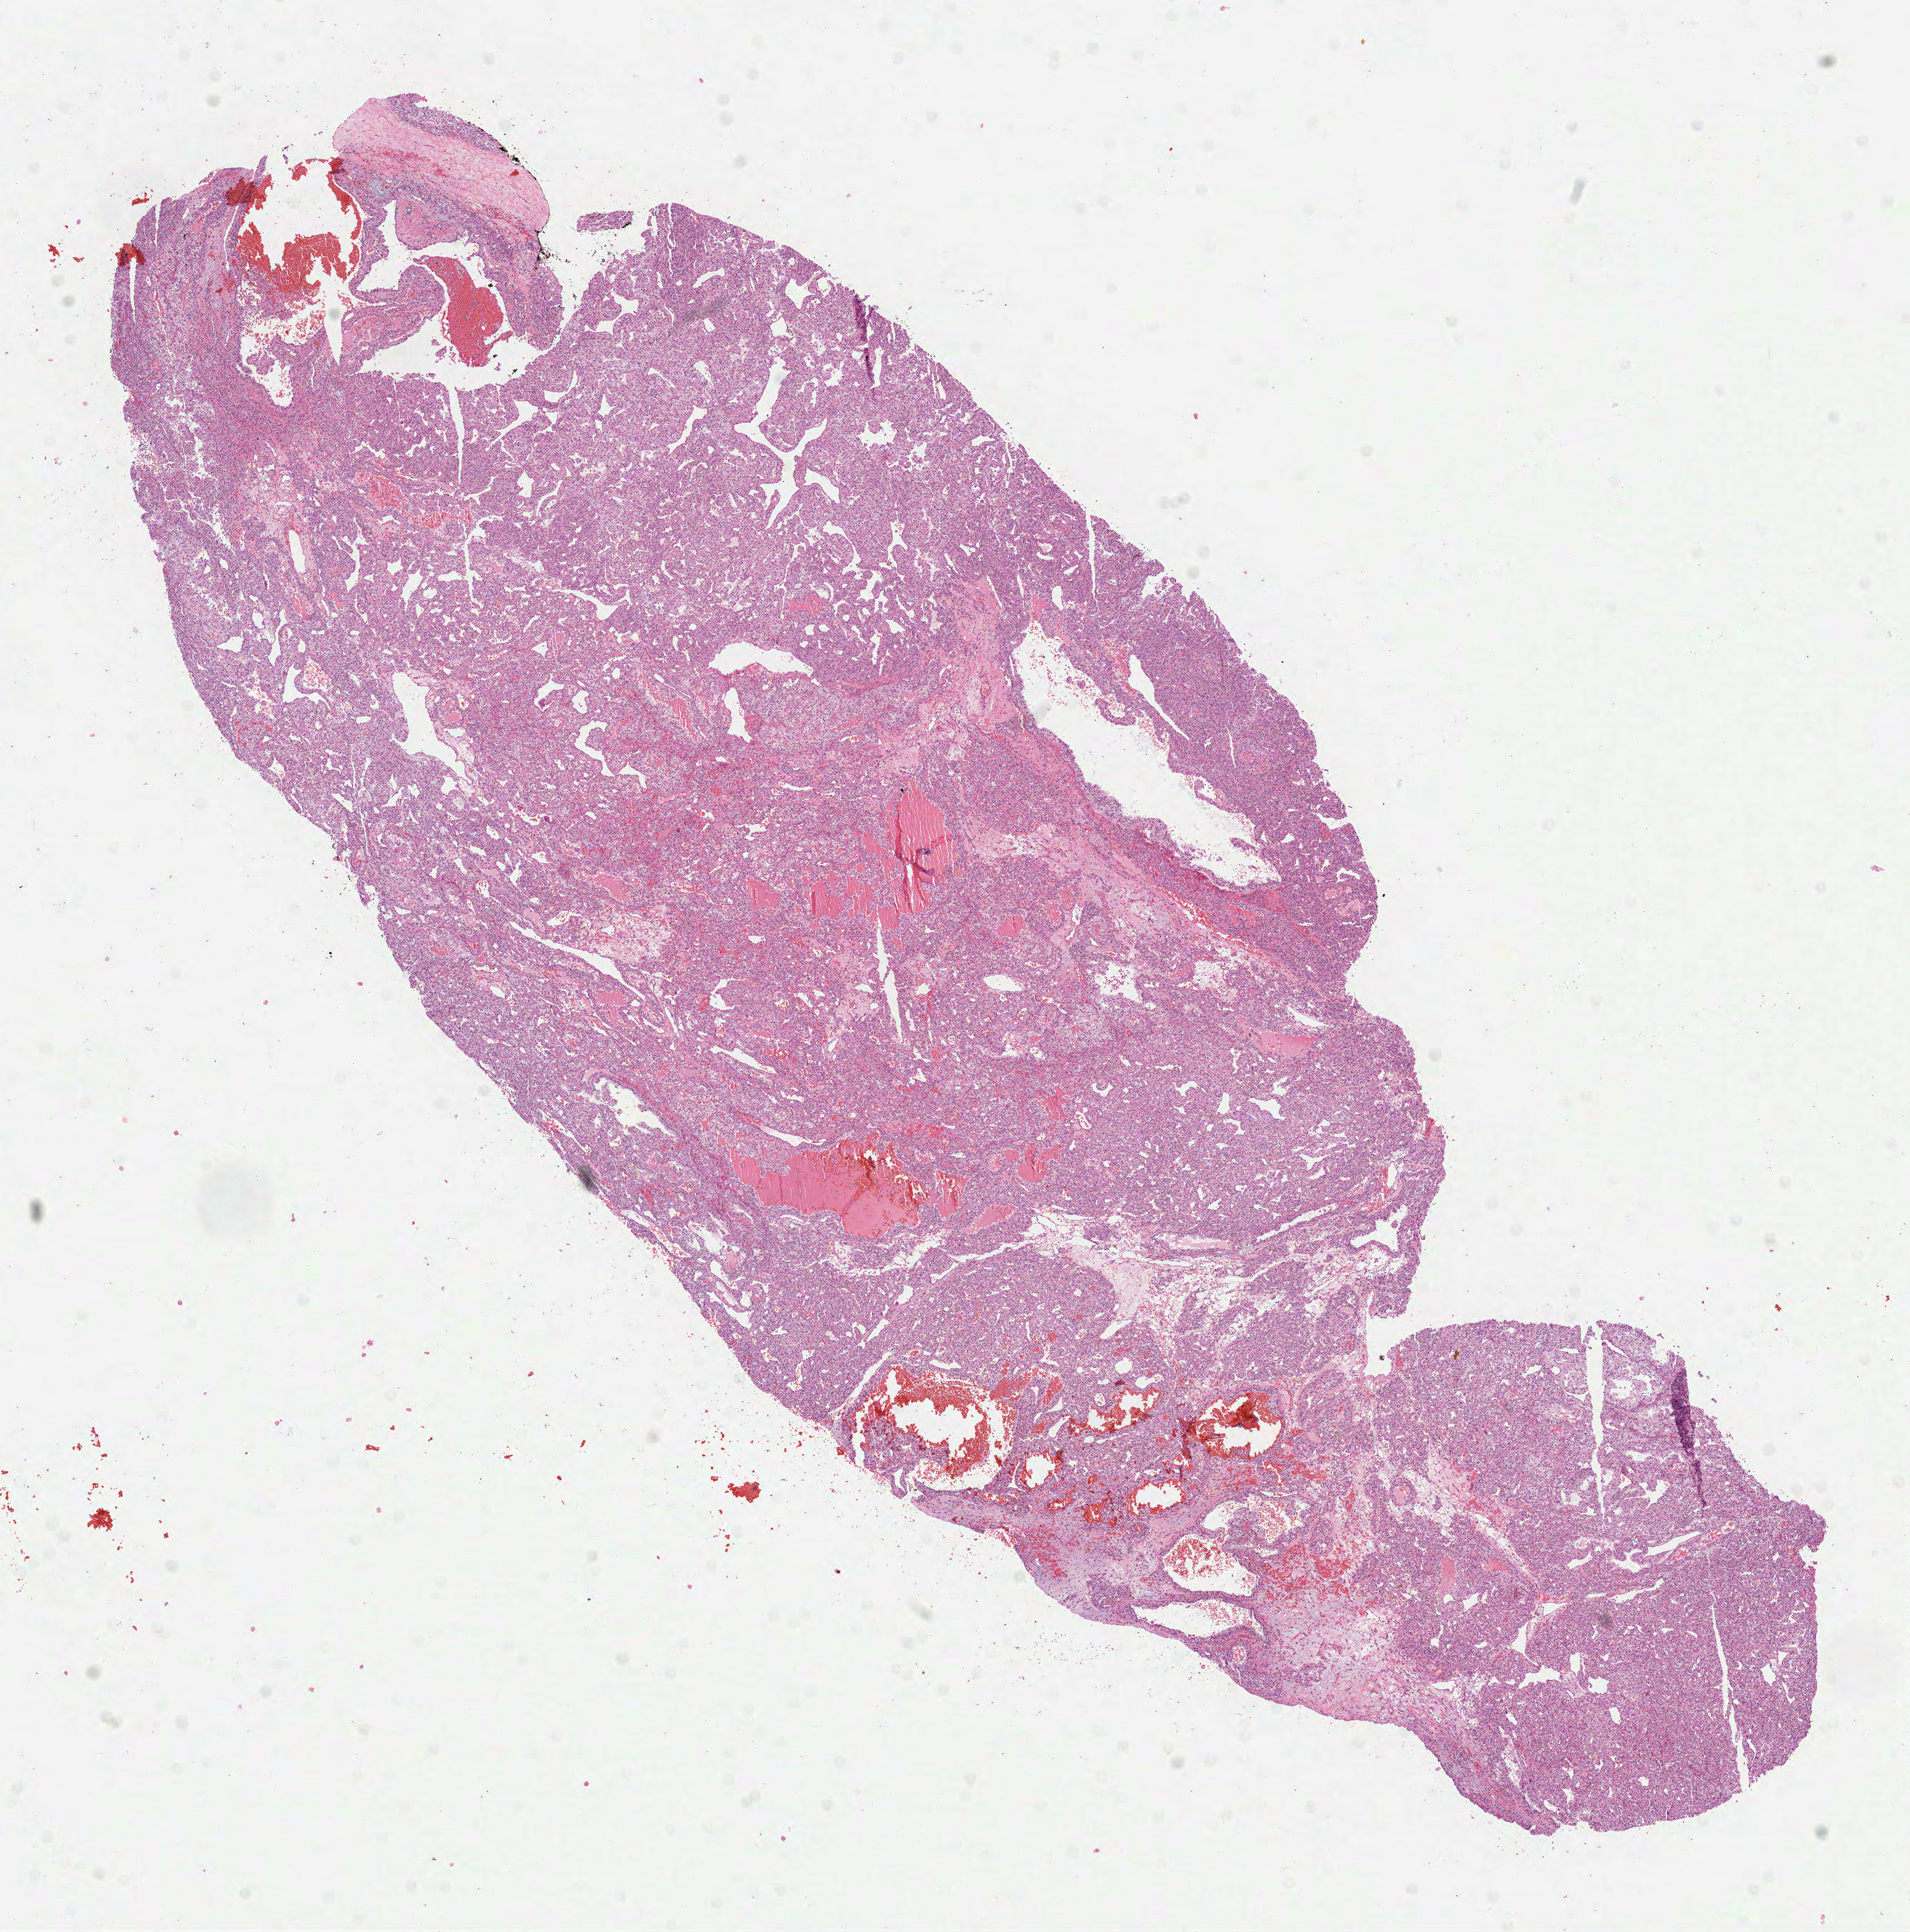
H&E whole-slide image, a low-resolution overview of the entire scanned area, about 12.3 x 12.5 mm (from a 40x scan). Formalin-fixed paraffin-embedded (FFPE) diagnostic section. Primary tumour sample from the kidney. Male patient; age at initial diagnosis 51 years. Histologic grade: G3 (poorly differentiated).
* AJCC pathologic stage: I
* histologic diagnosis: Clear cell adenocarcinoma, NOS
* laterality: right